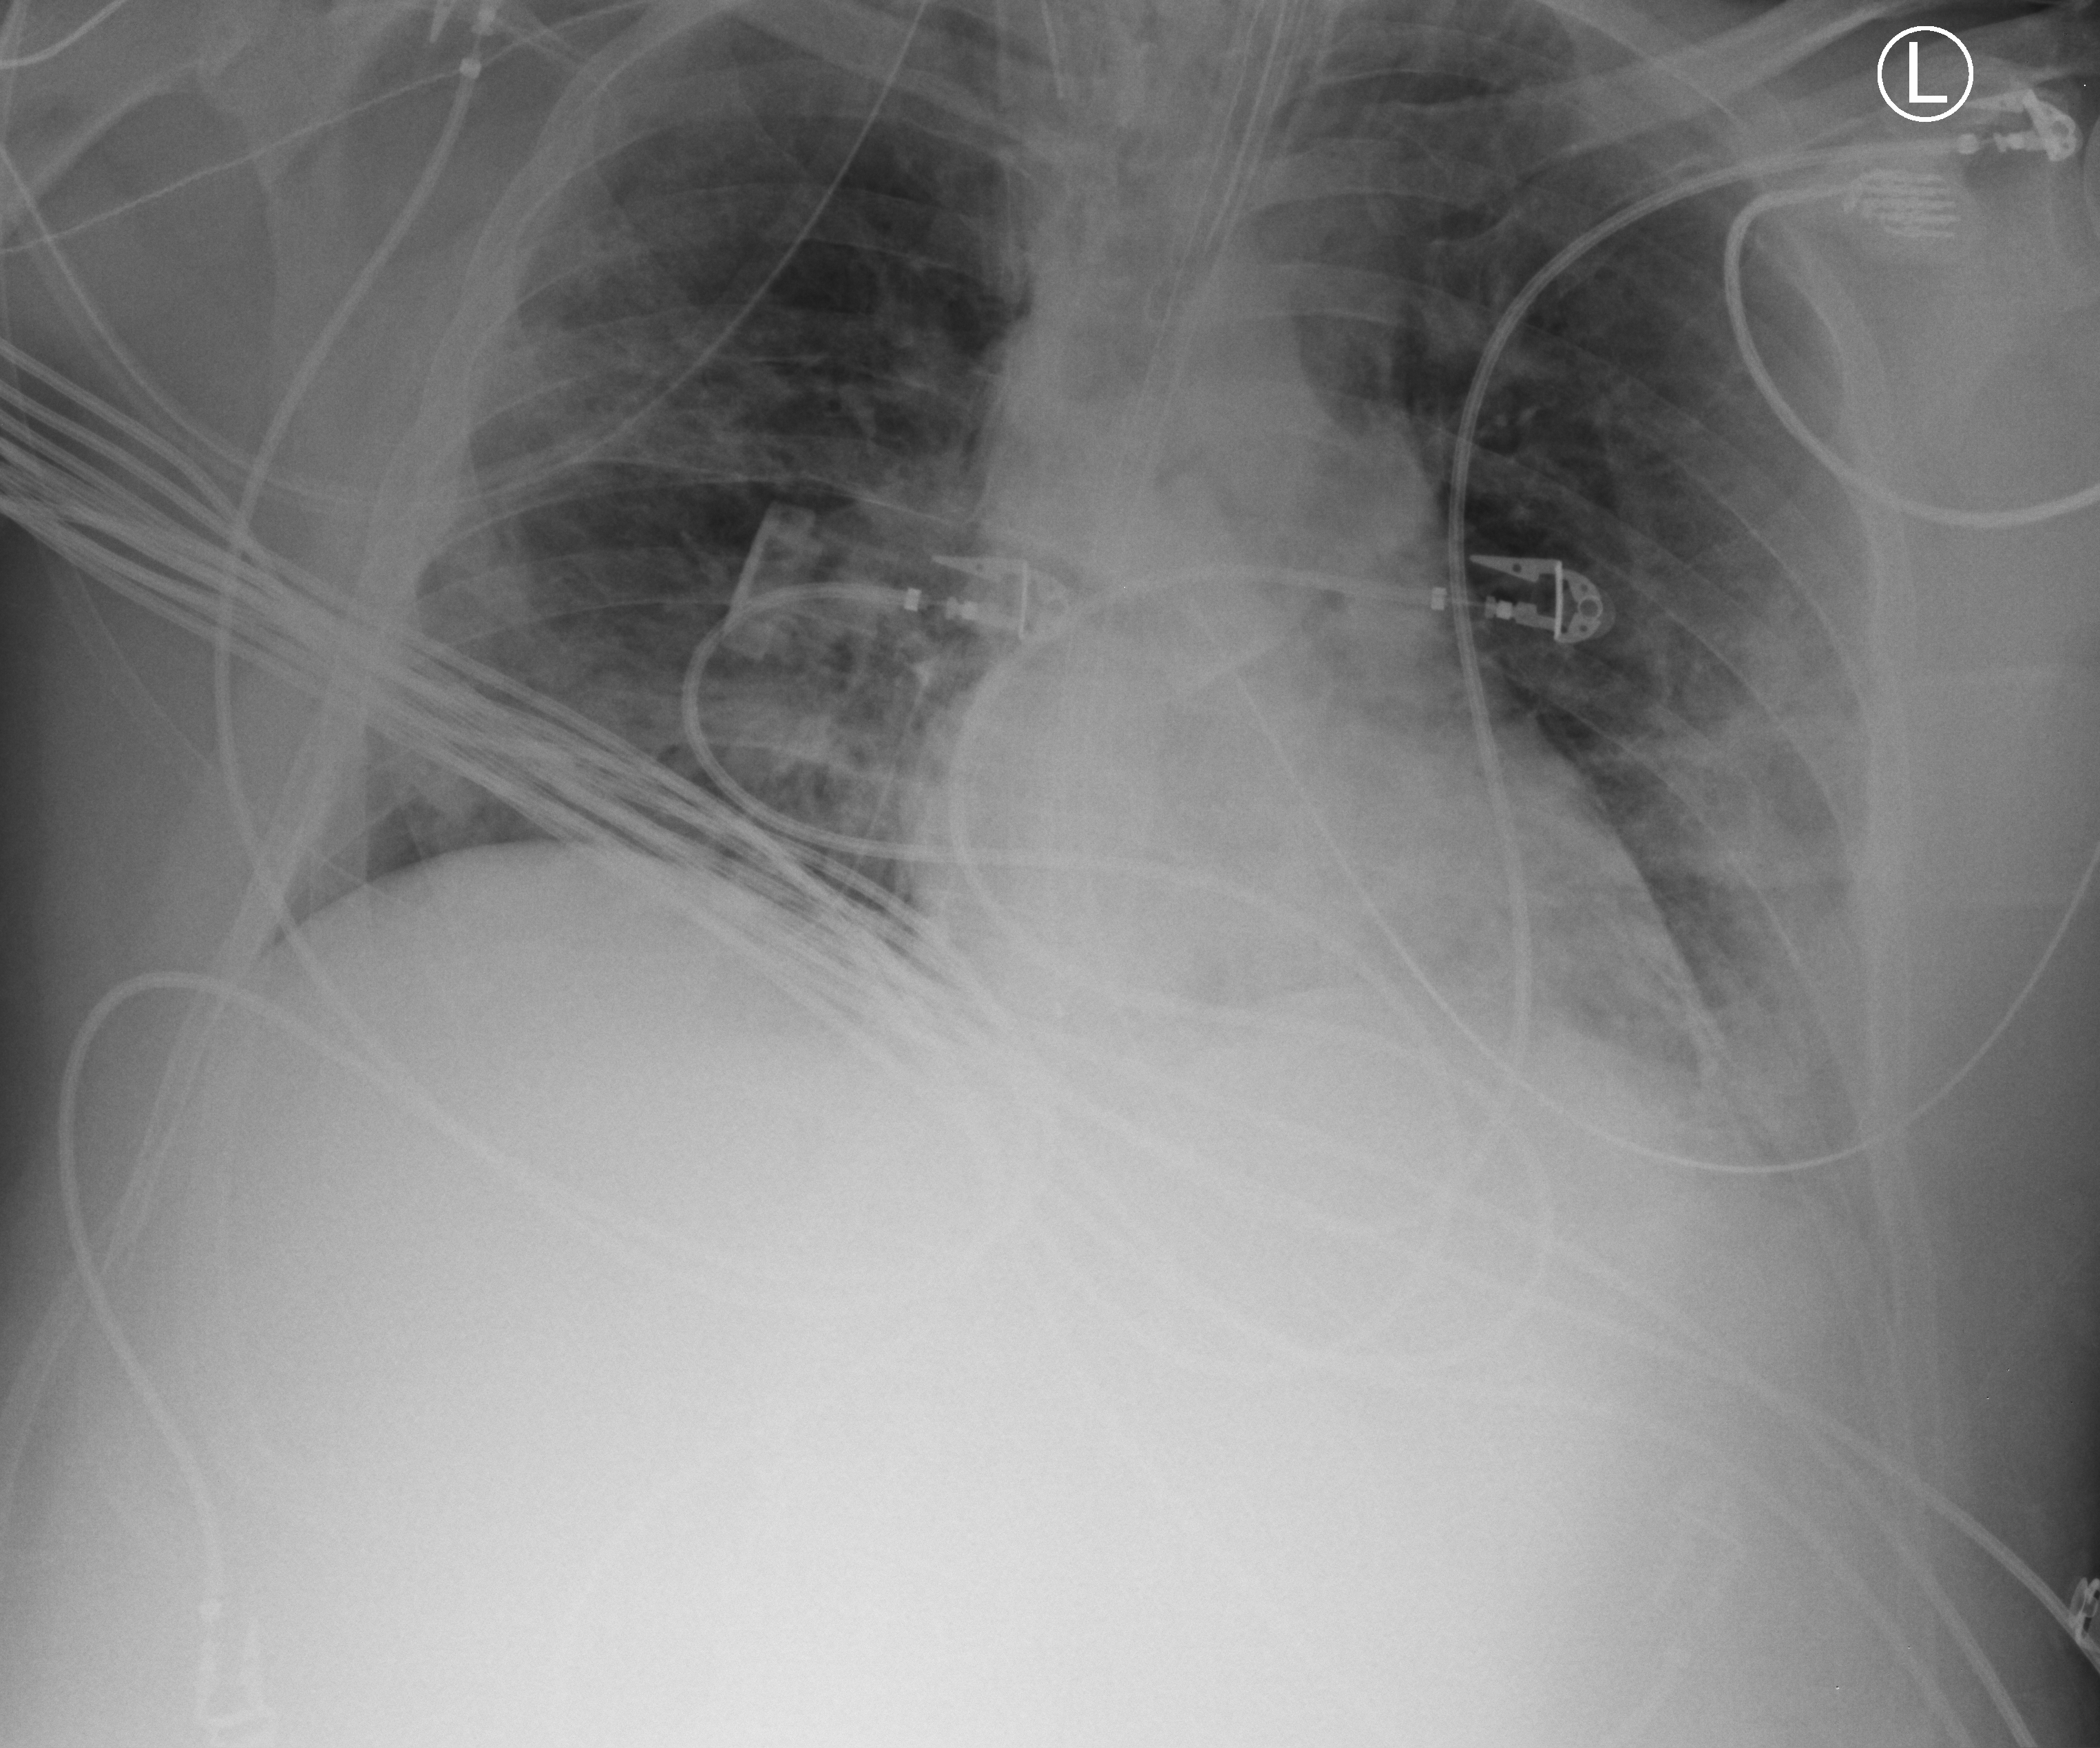
Chest X-ray (portable). Patient hospitalised with COVID-19, aged 18–59 years.
From the hospital-stay record, not from the radiograph (when in the stay this image was taken is not recorded): mechanically ventilated during this hospital stay: yes; admitted to intensive care during this hospital stay: yes.